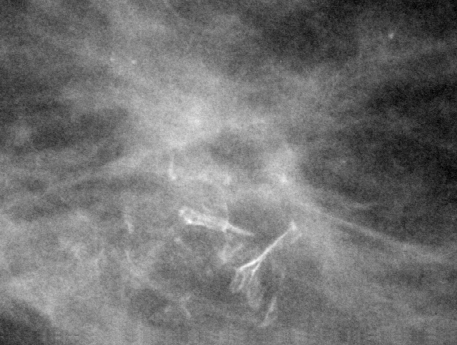
Cropped region of a digitized screen-film mammogram centred on a radiologist-marked abnormality, right breast, CC view.
- Finding: calcifications, morphology fine linear branching, distribution clustered; BI-RADS assessment category 4; subtlety rating 4 on a 1 (subtle) to 5 (obvious) scale; pathology (as recorded): benign.